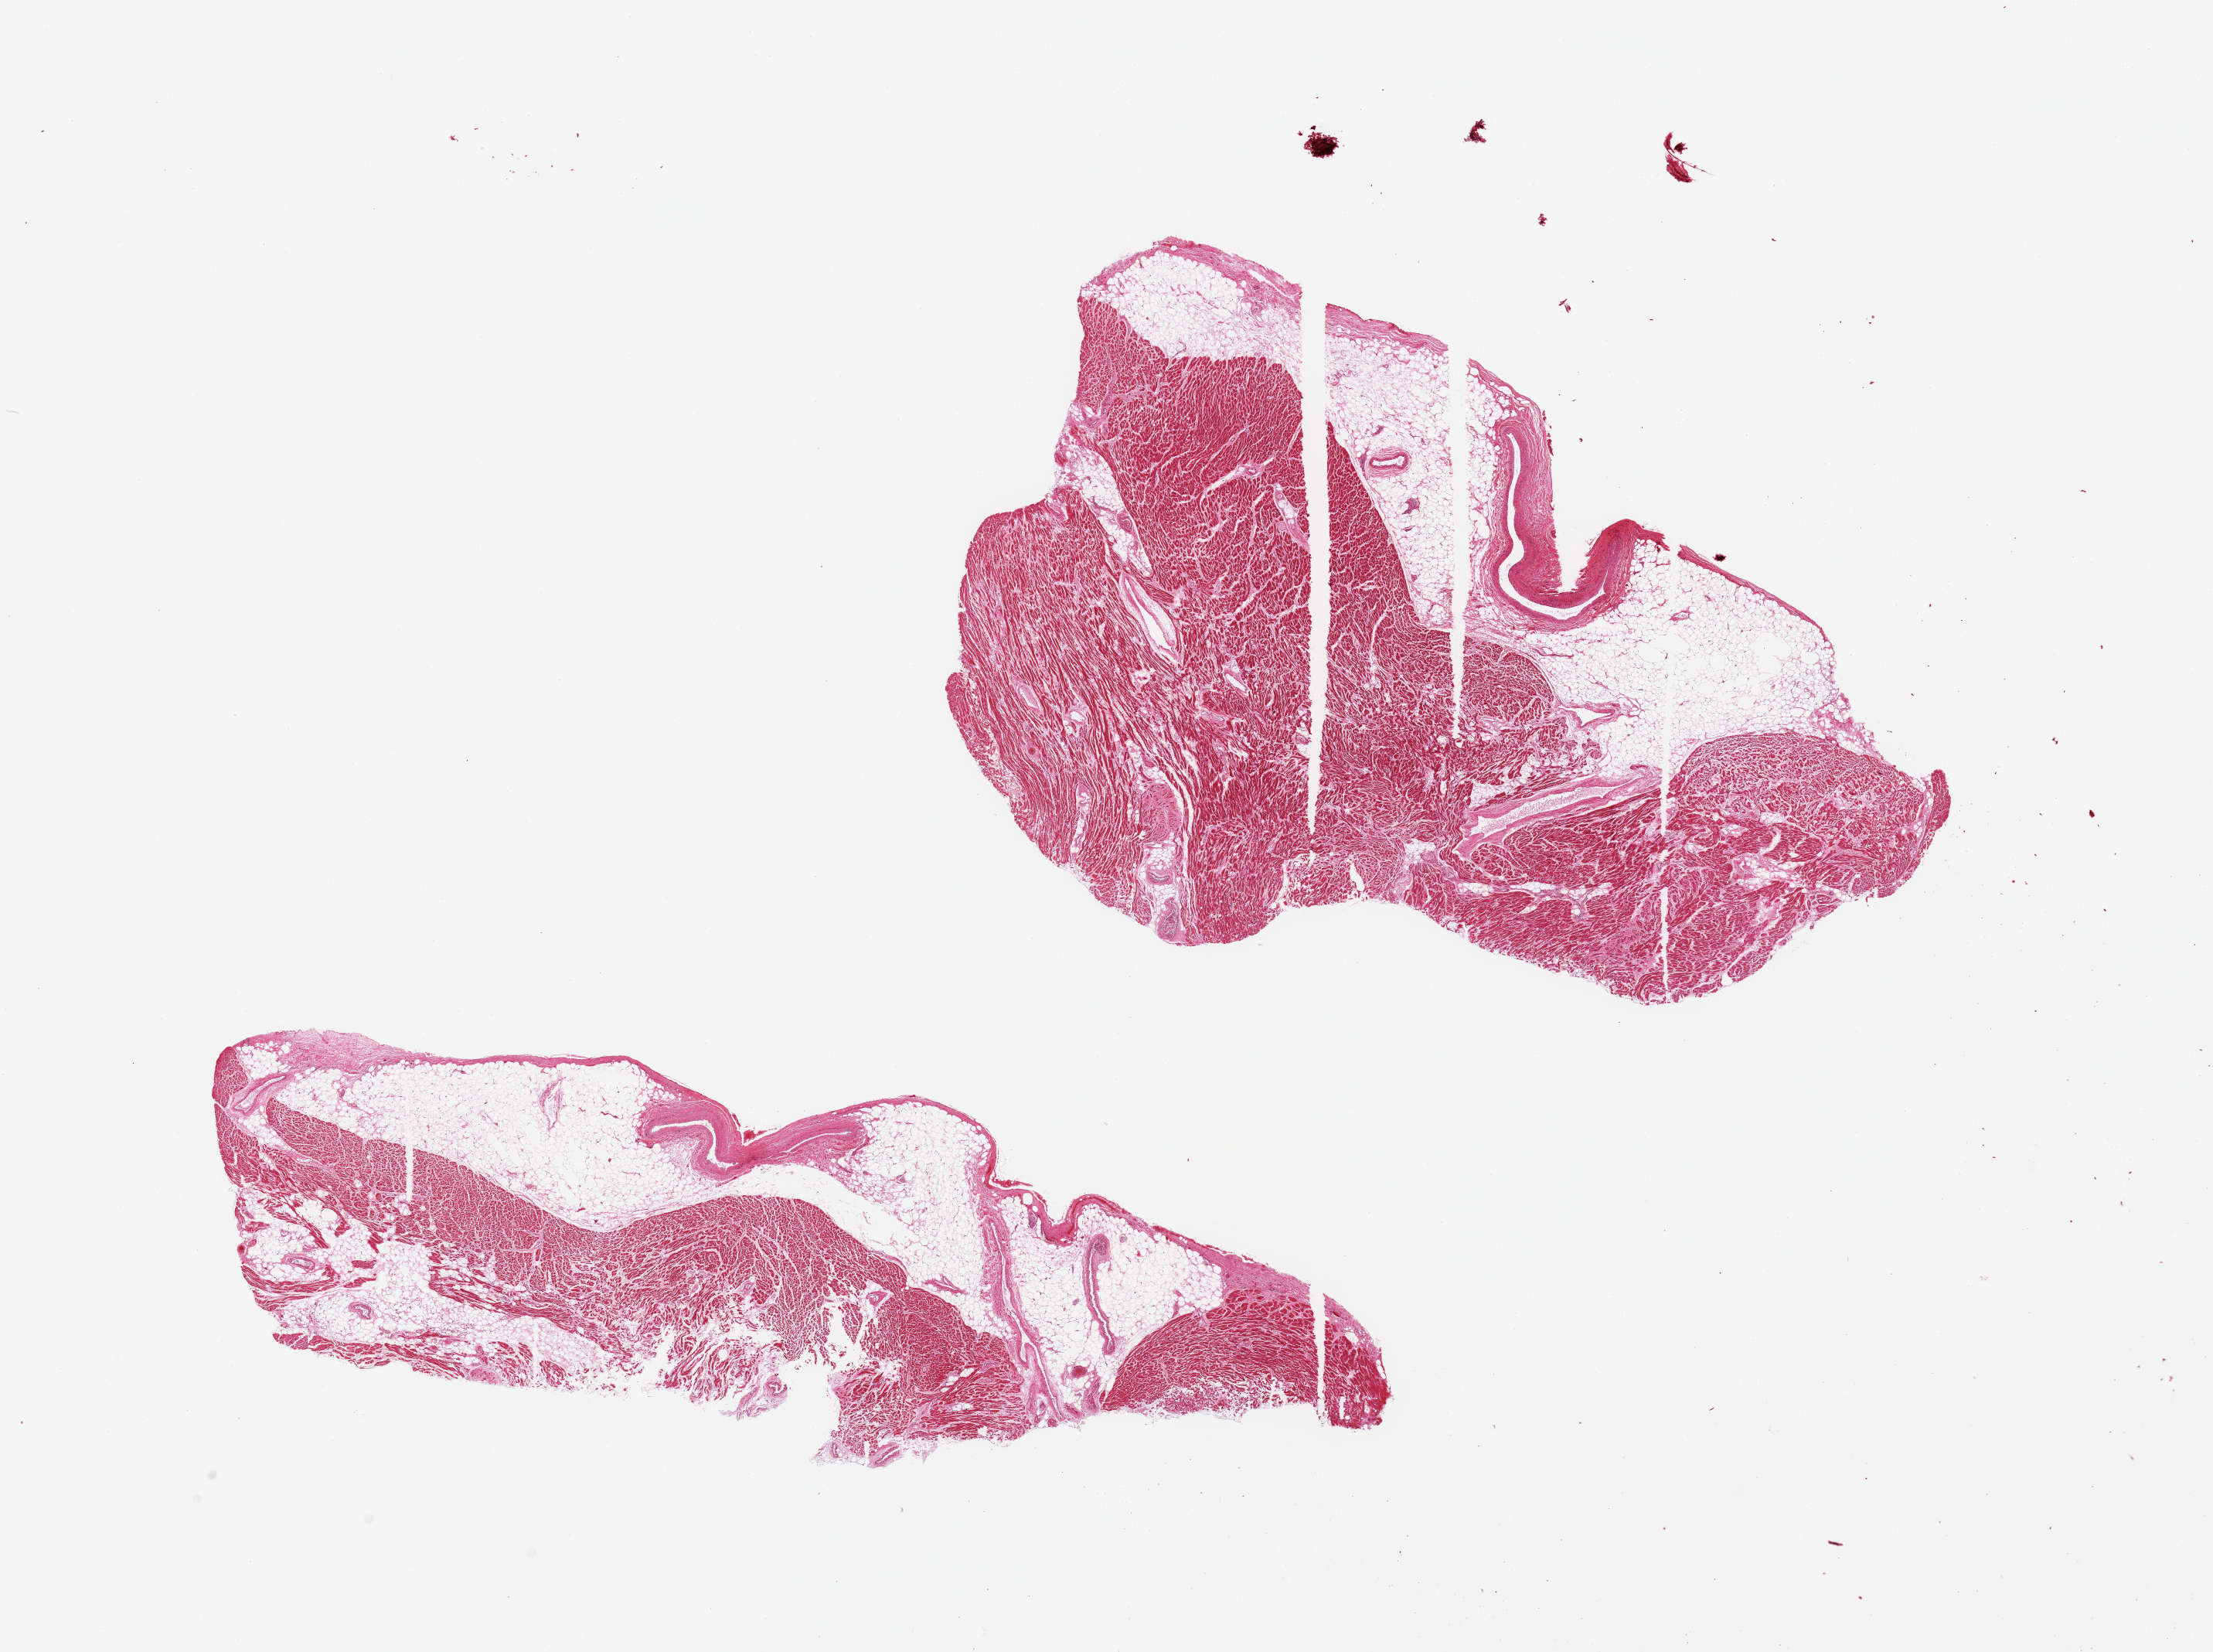
Whole-slide image, haematoxylin and eosin stain, brightfield, a low-resolution overview of the entire scanned area, about 22.6 x 16.9 mm (slide scanned at 20x); PAXgene-fixed paraffin-embedded (PFPE) section; section of coronary artery (target tissue); tissue donor sample. Male donor.
Review note (as recorded): 2 pieces; myocardium and fat comprise 90% of area; small arteries & veins present.